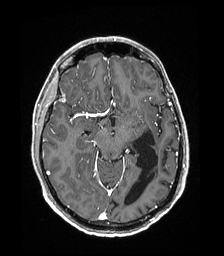
Brain MRI from a brain-tumour surgery series, one axial slice. Slice 108 of 192 in the series (ordered by position). T1-weighted post-contrast. 224 × 256 image matrix, field of view 224 × 256 mm. Case-level facts recorded for this patient, not image findings: histopathology: Low grade glioma; IDH mutation: no.
Outlined on this slice (expert manual segmentation):
- previous resection cavity: box from (x=125, y=131) to (x=158, y=205) px